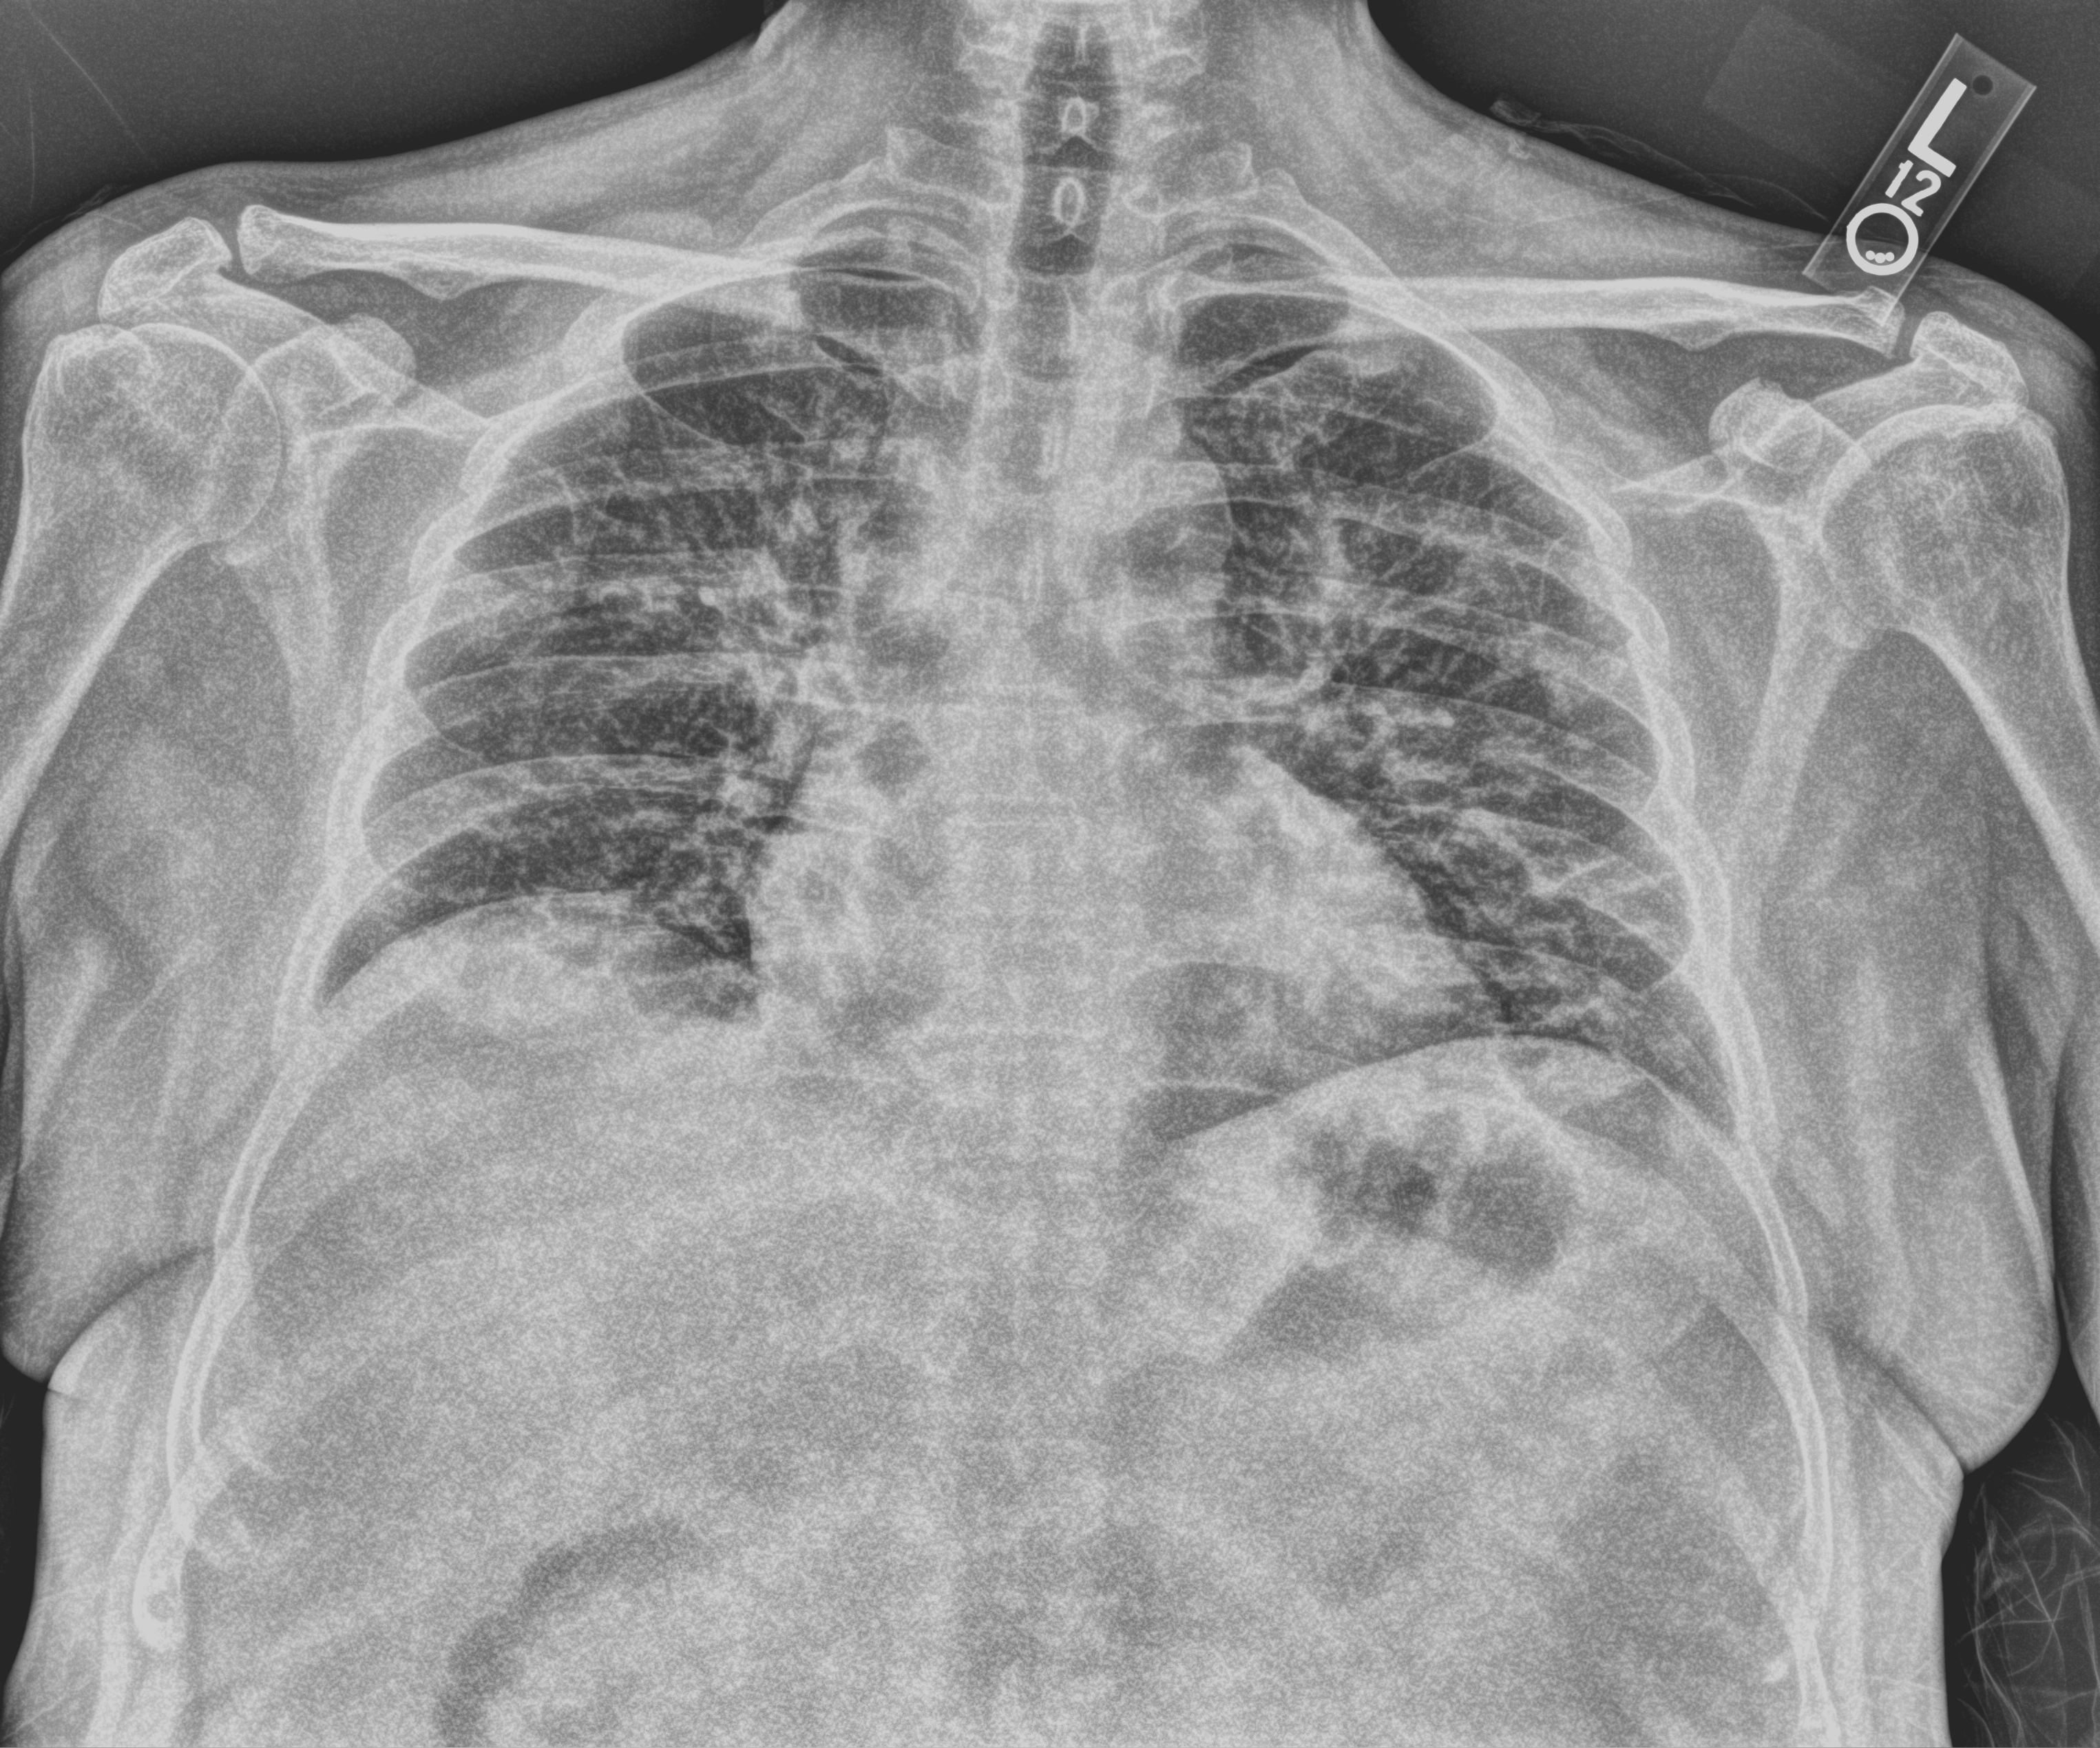
Portable chest radiograph, anteroposterior (AP) projection. Patient hospitalised with COVID-19; male, aged 18–59 years.
Hospital-stay facts (about this admission, not read from this image; timing relative to this image not recorded): hypertension (admission record): no; admitted to intensive care during this hospital stay: no.